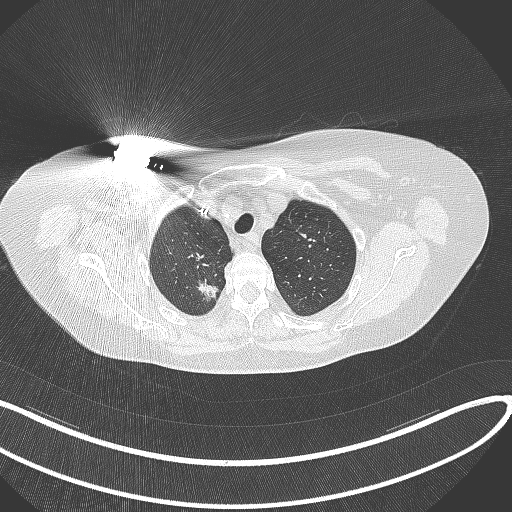
Chest CT, one axial slice; position 279 of 316 along the scan axis; lung window (W 1500 / L -600 HU); 512 × 512 image matrix, field of view 400 × 400 mm. Female patient, age 72 years. From the clinical record (not read from this slice): clinical TNM (as recorded): T1c N0 M0.
Annotated regions visible in this slice (rectangle marked by the reading radiologist):
- lung tumour (recorded histology: adenocarcinoma): box from (x=195, y=275) to (x=222, y=301) px